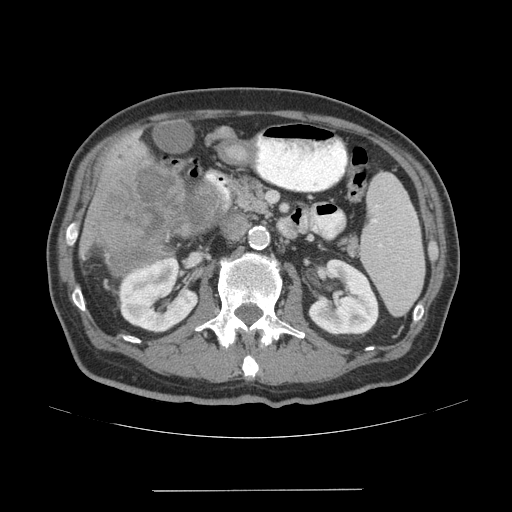
Contrast-enhanced abdominal CT (liver protocol), one axial slice; slice 13 of 77 in the series (ordered by position); reconstruction kernel STANDARD; 140 kVp; soft-tissue window (W 400 / L 40 HU); 2.5 mm slice thickness; 512 × 512 image matrix. From the clinical record (not read from this slice): diagnosis: hepatocellular carcinoma (patient treated with transarterial chemoembolisation; whether this scan precedes or follows treatment is not stated here); TNM stage (as recorded): Stage-IVA; Child-Pugh class: A; tumour nodularity: uninodular.
Annotated regions visible in this slice (semi-automatically segmented with operator editing):
- liver parenchyma outside the tumour (the mass and vessels are separate outlines, so this box may not span the whole liver): bounding box (x1, y1, x2, y2) in pixels: (80, 134, 154, 276)
- mass: (91, 162, 223, 275)